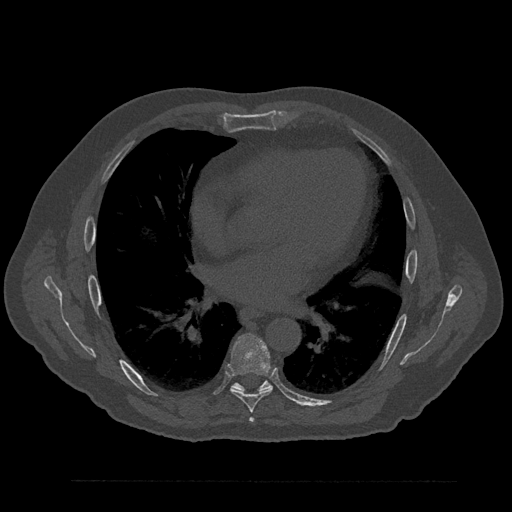
CT including the spine, one axial slice; slice 490 of 797 in the series (ordered by position); reconstruction kernel Br40s/3; 120 kVp; bone window (W 1800 / L 400 HU); 0.5 mm slice thickness; 512 × 512 image matrix, field of view 430 × 430 mm. Patient: male, 61 years. Case-level facts recorded for this patient, not image findings: primary cancer: prostate.
Outlined on this slice (semi-automatic segmentation, software-assisted and operator-edited):
- T6 vertebra: bounding box [x1, y1, x2, y2] px = [250, 418, 254, 422]
- T7 vertebra: [228, 335, 273, 413]
- T8 vertebra: [232, 381, 272, 392]